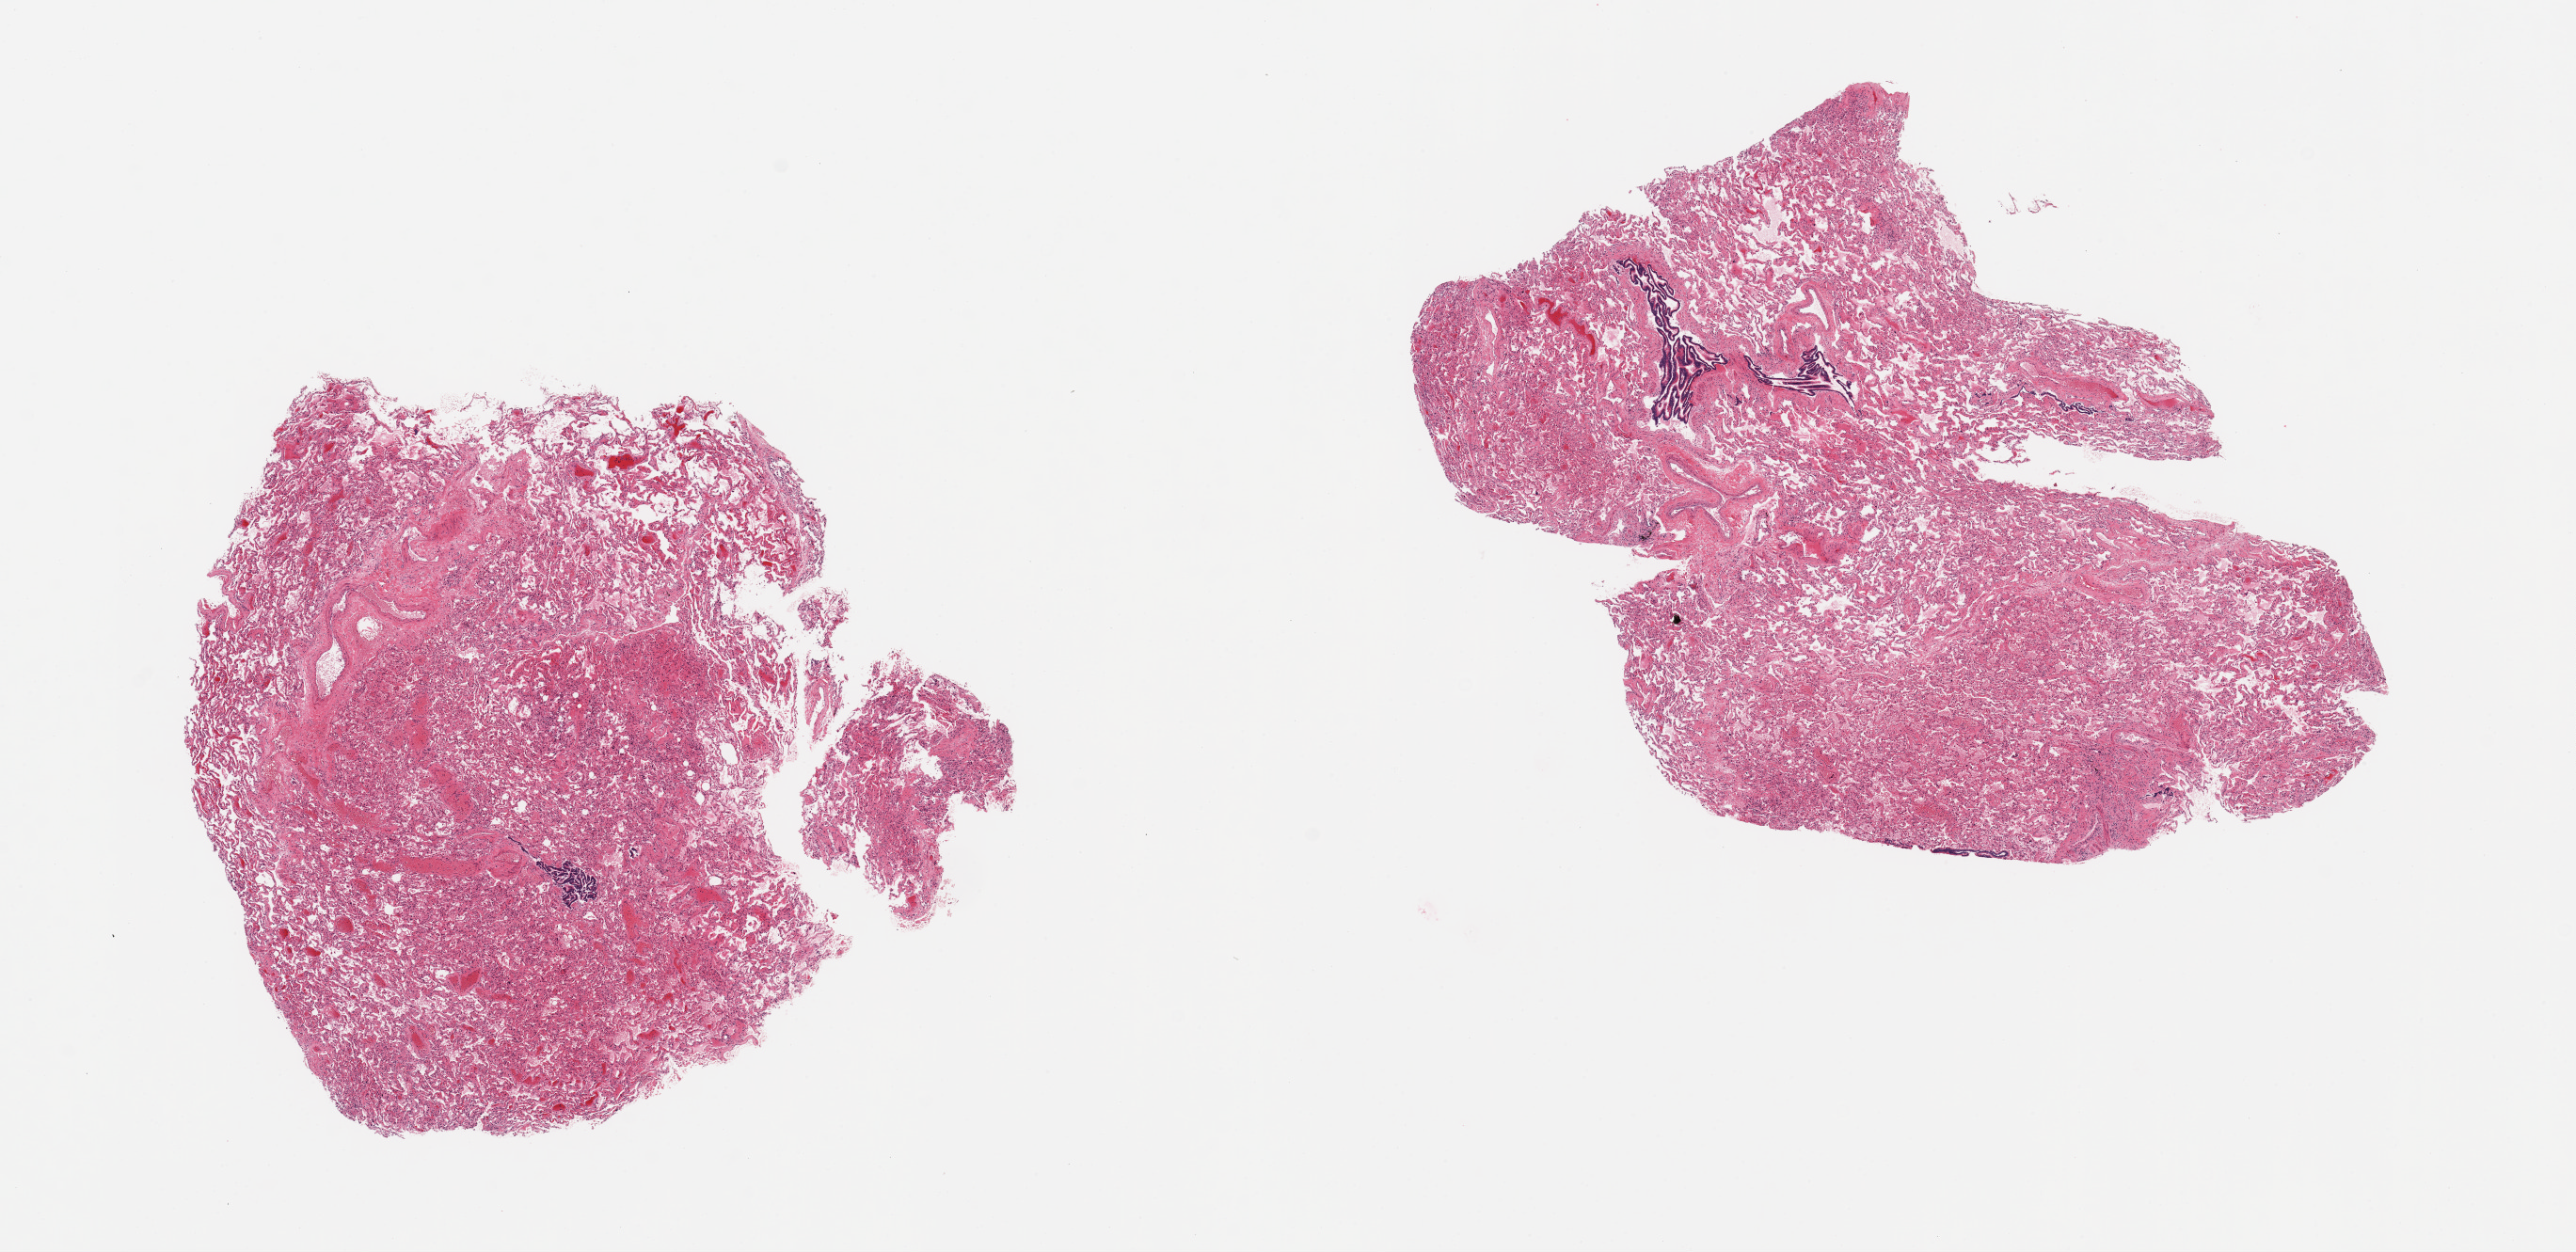
Whole-slide image, hematoxylin and eosin (H&E) stain, shown as a low-resolution overview of the whole scanned area (about 21.7 x 10.5 mm, slide scanned at 20x). PAXgene-fixed paraffin-embedded (PFPE) section. Target tissue: lung. Tissue donor sample. Donor sex: male.
Reviewer comment on this tissue sample: 2 pieces; 1 piece with large bronchus [10%].